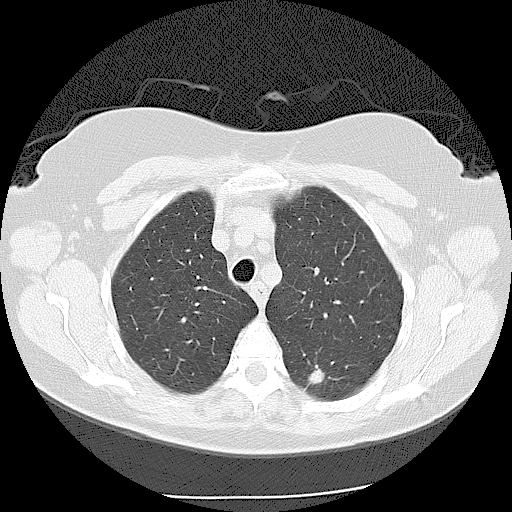
Low-dose screening chest CT, one axial slice. Position 88 of 116 along the scan axis. Lung window (W 1500 / L -600 HU). 2.5 mm slice thickness. 512 × 512 image matrix.
Annotated regions visible in this slice (expert manual segmentation):
- lesion 1 (tumor, lower lobe of left lung): bounding box (x1, y1, x2, y2) in pixels: (308, 365, 325, 385)